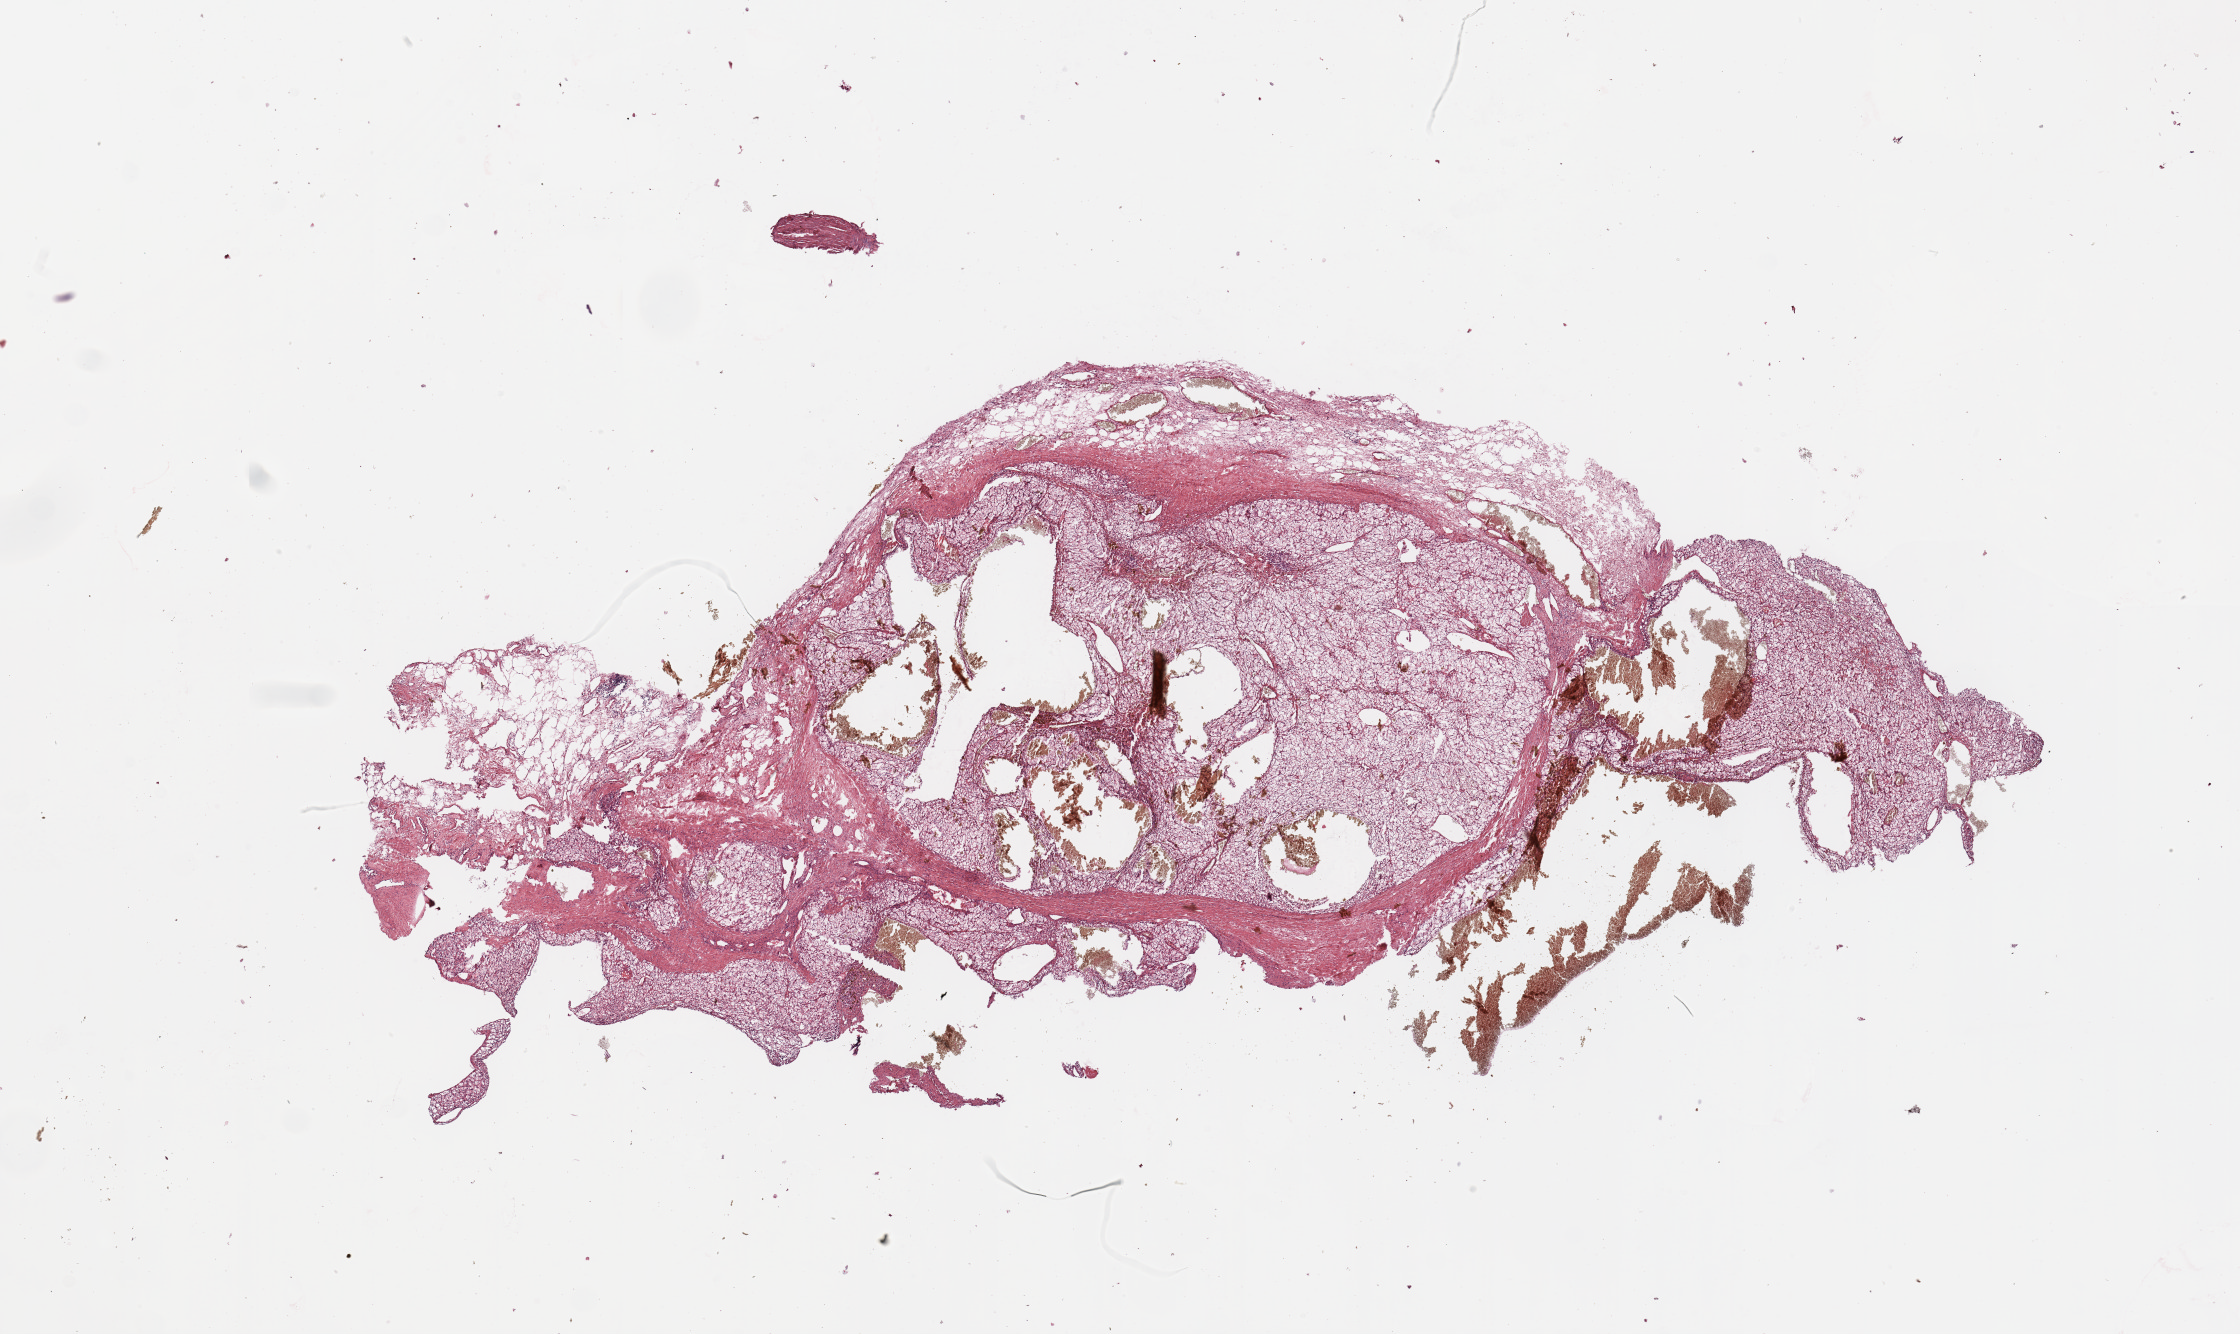
Whole-slide histology image, H&E, a low-resolution overview of the entire scanned area, about 17.7 x 10.6 mm (acquisition: 20x scan). Kidney, tumour tissue. 67-year-old female patient. Histologic grade: G2 (moderately differentiated).
Histologic diagnosis: Renal cell carcinoma, NOS. Primary tumour site (as recorded): lower pole. AJCC pathologic stage: IV.